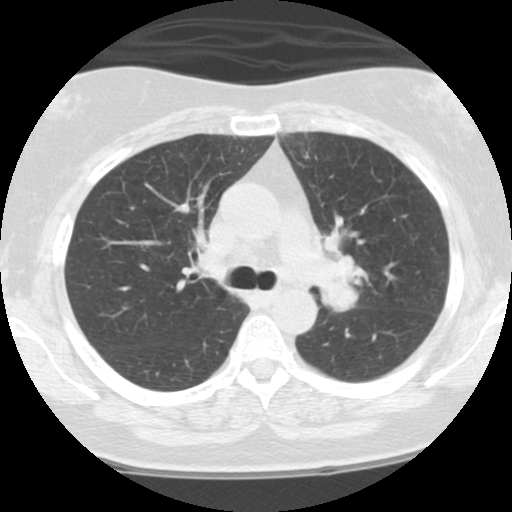
Low-dose screening chest CT, one axial slice; slice 73 of 108 in the series (ordered by position); lung window (W 1500 / L -600 HU); 512 × 512 image matrix, field of view 300 × 300 mm.
Structures marked on this image (outlined manually by an expert reader):
- lesion 1 (tumor, hilum of left lung): bounding box (x1, y1, x2, y2) in pixels: (319, 258, 367, 312)